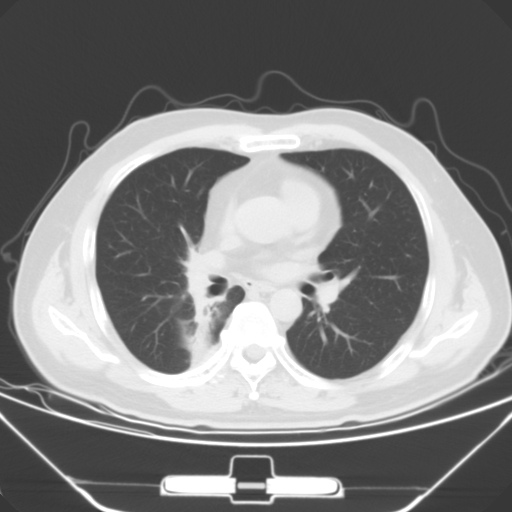
Chest CT, one axial slice; slice 29 of 56 in the series (ordered by position); 120 kVp; lung window (W 1500 / L -600 HU); 5 mm slice thickness; 512 × 512 image matrix, field of view 371 × 371 mm. Male patient, age 48 years. Case-level facts recorded for this patient, not image findings: clinical TNM (as recorded): T1a N1 M1c.
Outlined on this slice (bounding box drawn by a radiologist):
- lung tumour (recorded histology: adenocarcinoma): box from (x=178, y=242) to (x=219, y=324) px